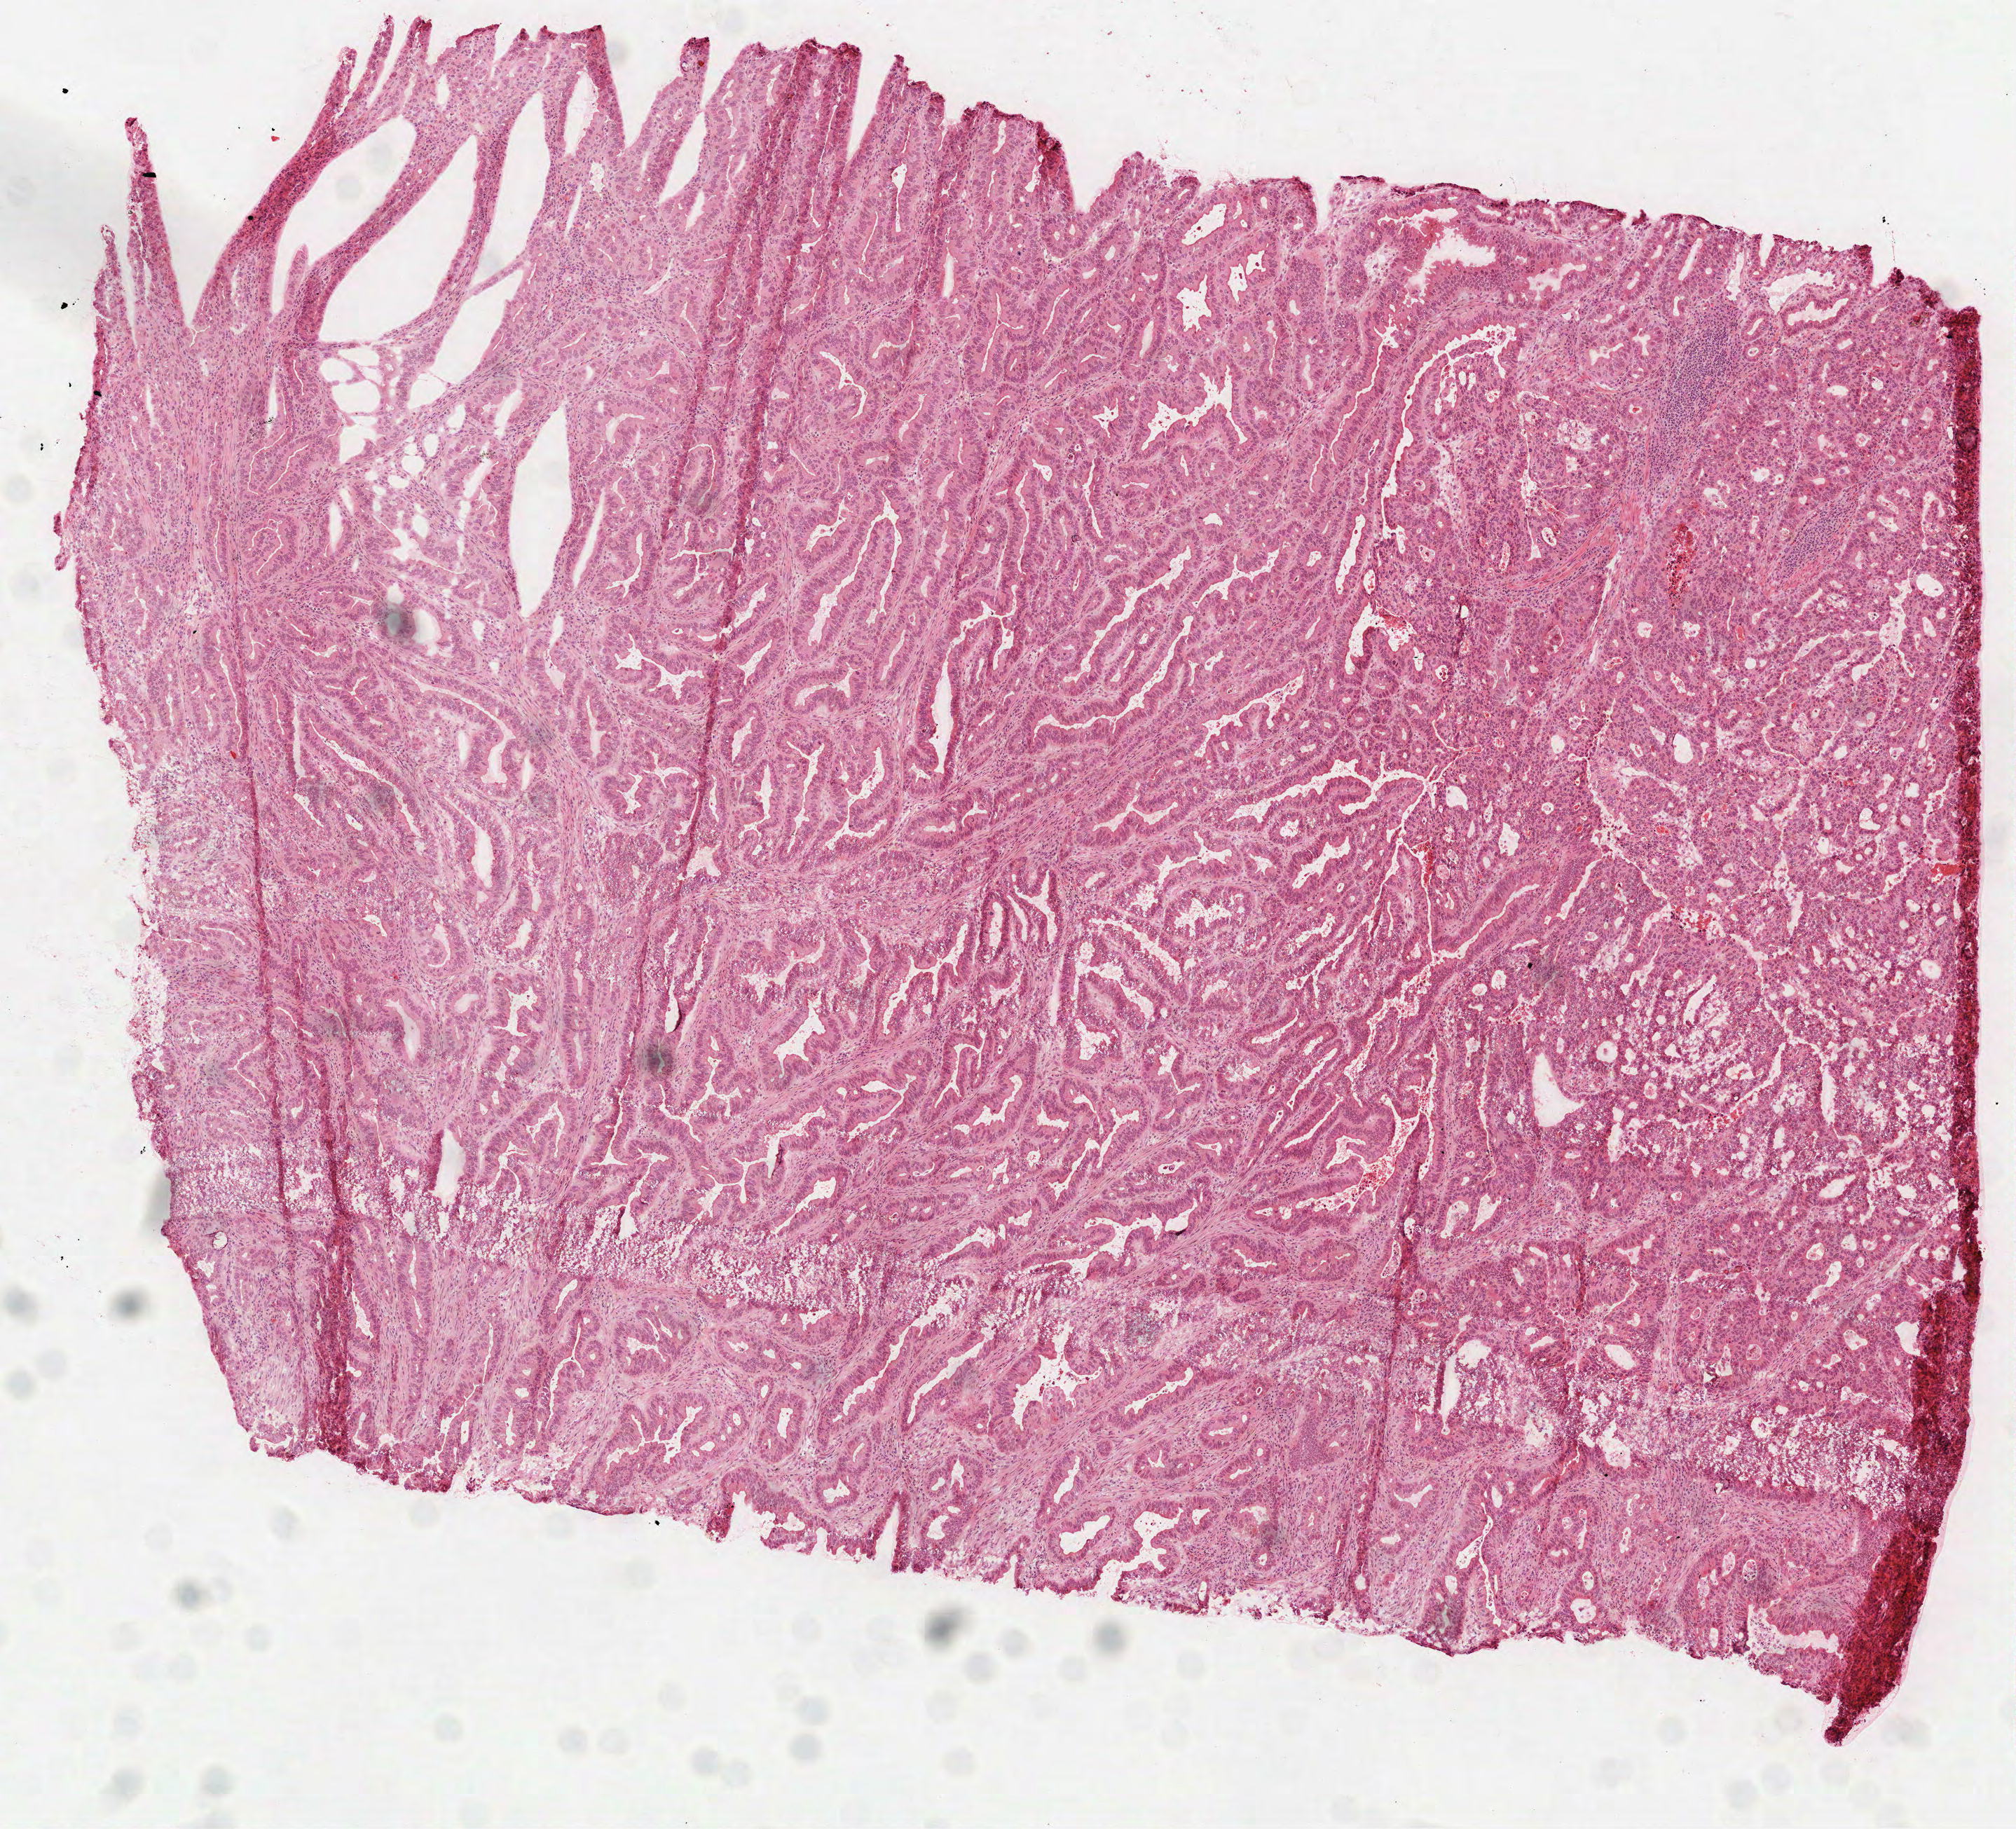
Hematoxylin and eosin (H&E) stained whole-slide image — shown as a low-resolution overview of the whole scanned area (about 5.8 x 5.3 mm, slide scanned at 40x); frozen section; sample: primary tumour, stomach. Female, age 70 years at initial diagnosis. Histologic grade: G2 (moderately differentiated). Pathologist review of this section (percent, as recorded): tumour cells 83%, tumour nuclei 80%, normal cells 0%, stromal cells 12%, necrosis 5%.
Lymph nodes positive (case pathology): 5 of 19 examined. Histologic diagnosis: Tubular adenocarcinoma (body of stomach). AJCC pathologic stage: IIB (7th edition).